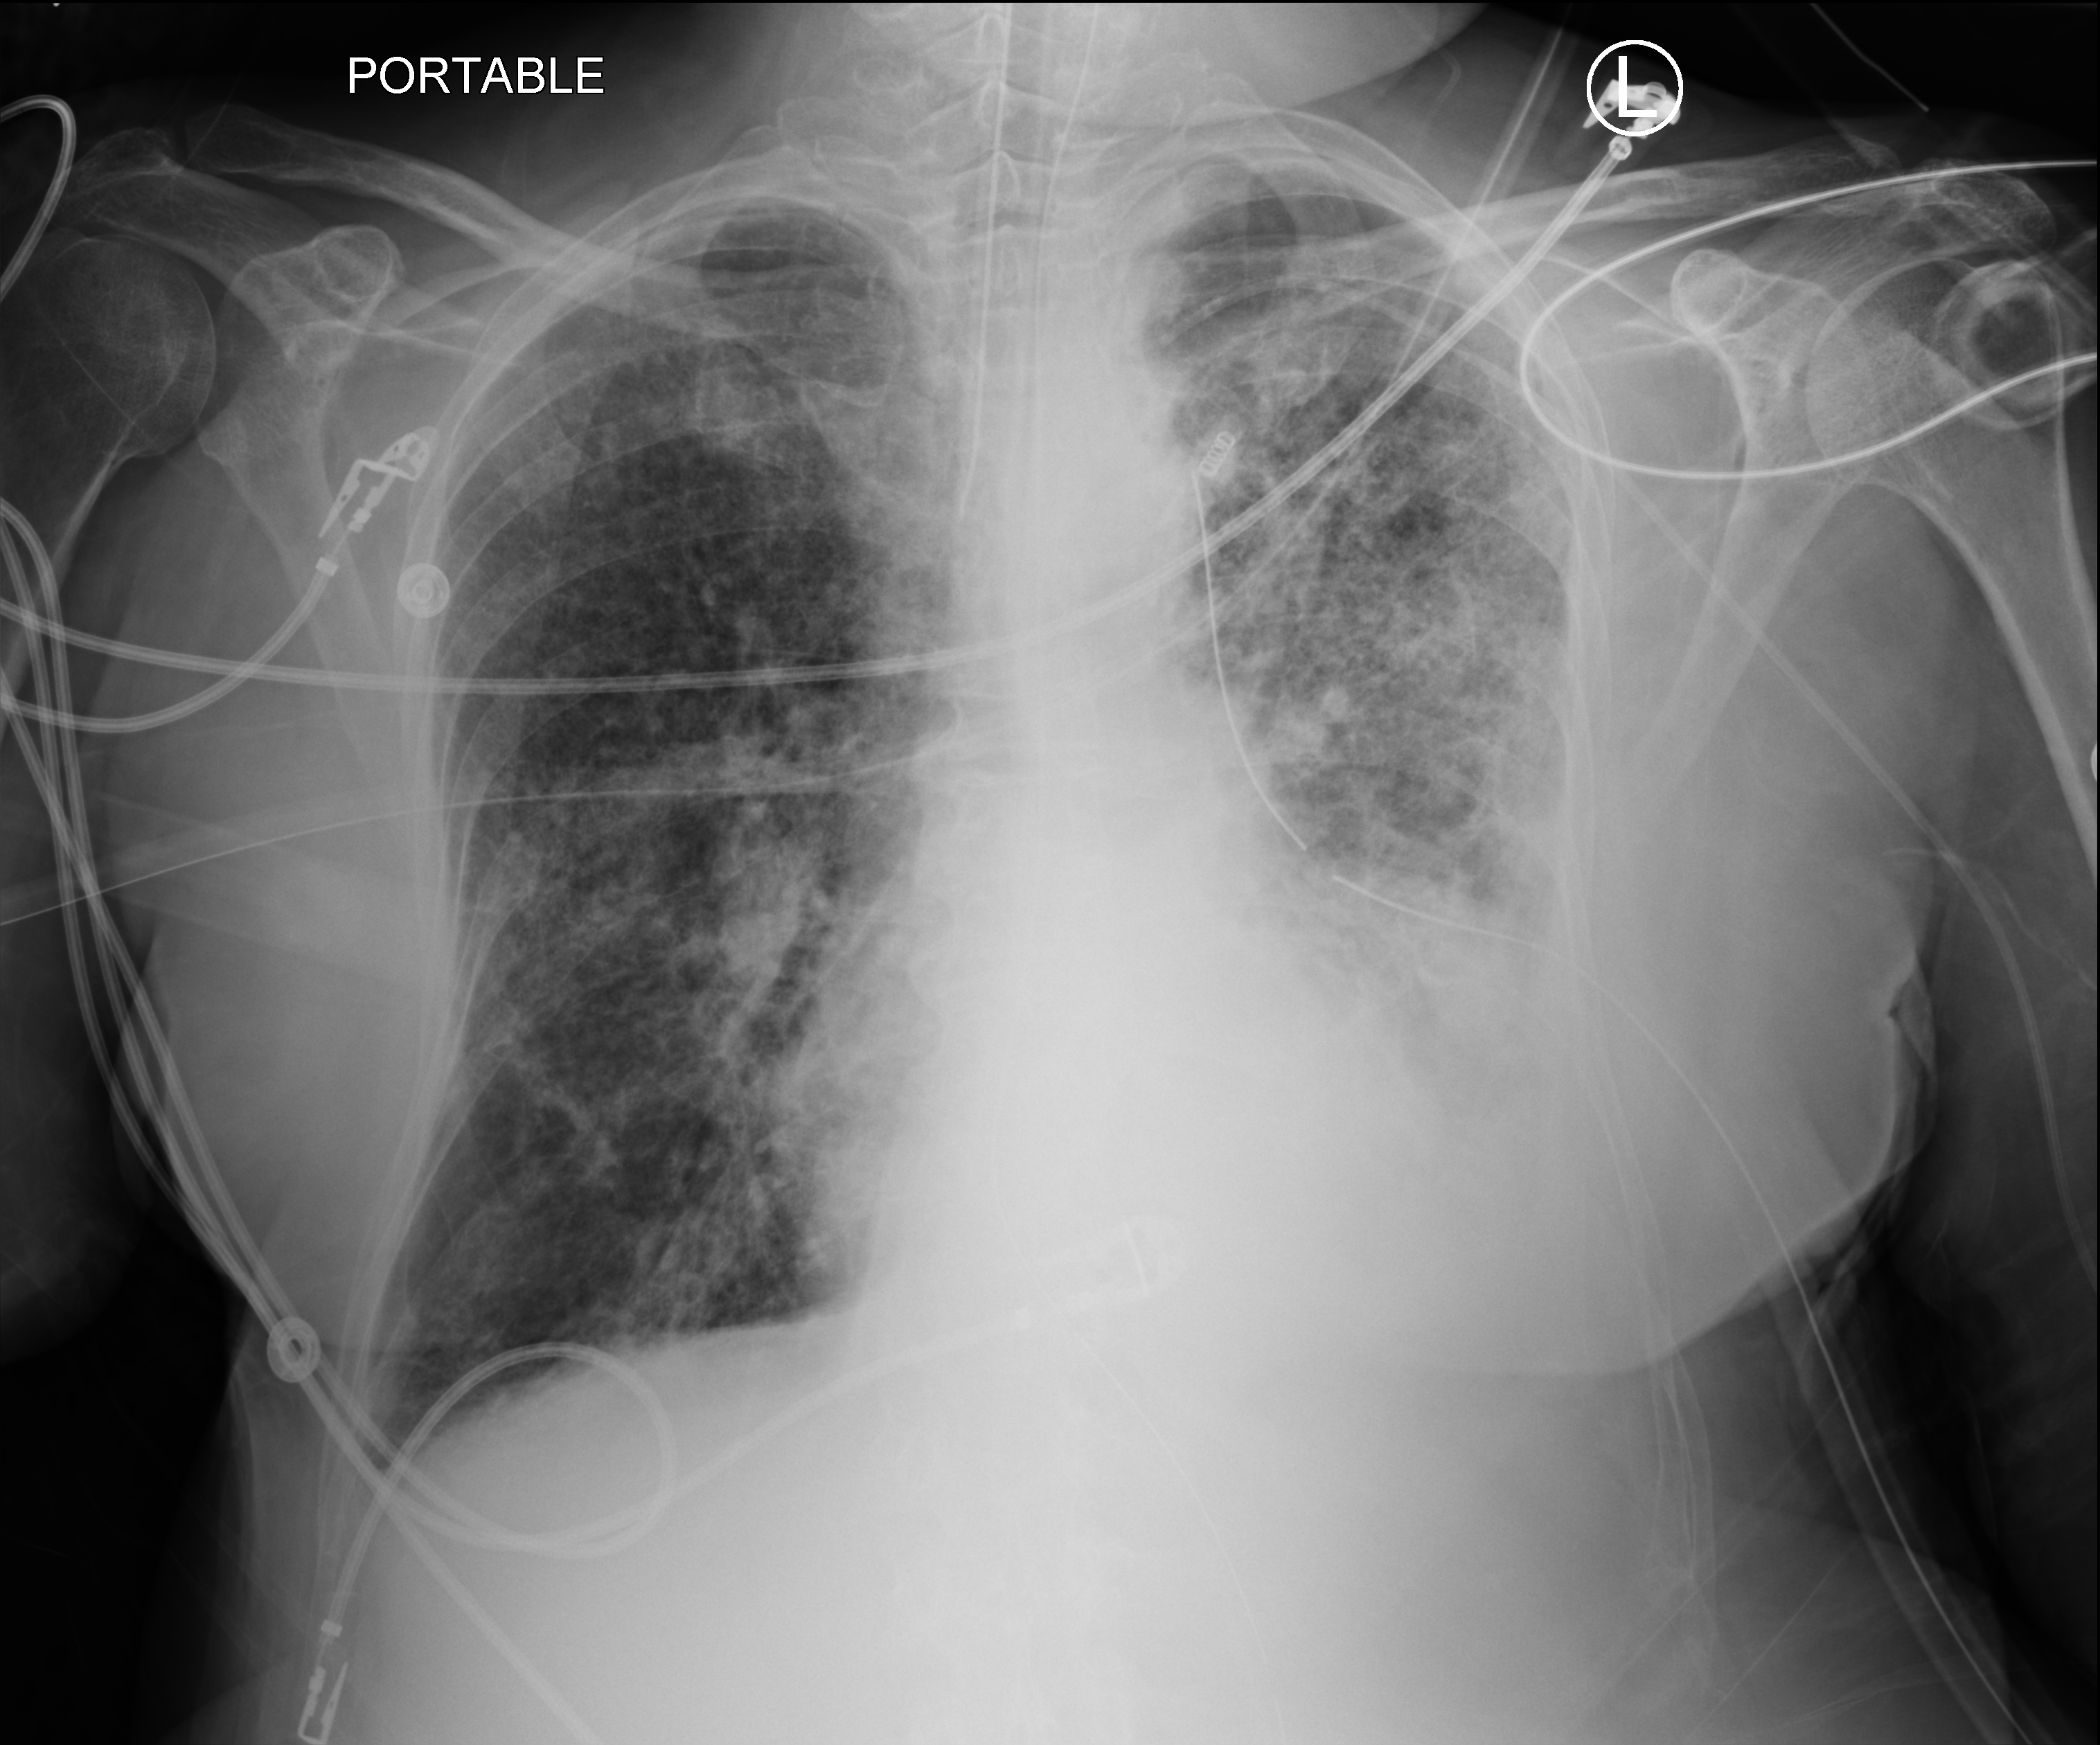
Chest X-ray (portable); anteroposterior (AP) projection. Female patient hospitalised with COVID-19, age 75–90 years.
Hospital-stay facts (about this admission, not read from this image; timing relative to this image not recorded): length of hospital stay: 70 days; admitted to intensive care during this hospital stay: yes.